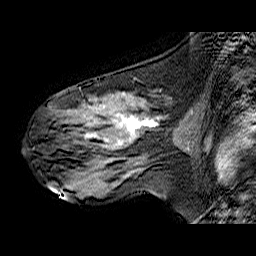
Breast MRI (dynamic contrast-enhanced), one sagittal slice; slice 34 of 60 in the series (ordered by position); dynamic contrast-enhanced series, time point 2 of 6 at this slice position (early post-contrast); 1.5 T; TE 6.3 ms, TR 32.9 ms; 256 × 256 image matrix, field of view 200 × 200 mm. Female patient. Case-level facts recorded for this patient, not image findings: setting: breast cancer imaged before/during neoadjuvant chemotherapy; receptor status: HER2-positive.
Structures marked on this image (semi-automatically segmented with operator editing):
- analysis volume of interest (the breast-tissue region the enhancement analysis was run in; not a lesion): bounding box [x1, y1, x2, y2] px = [34, 88, 174, 173]
- tumour enhancement mask (voxels above the 100 % enhancement threshold inside the analysis volume of interest): [86, 105, 158, 144]